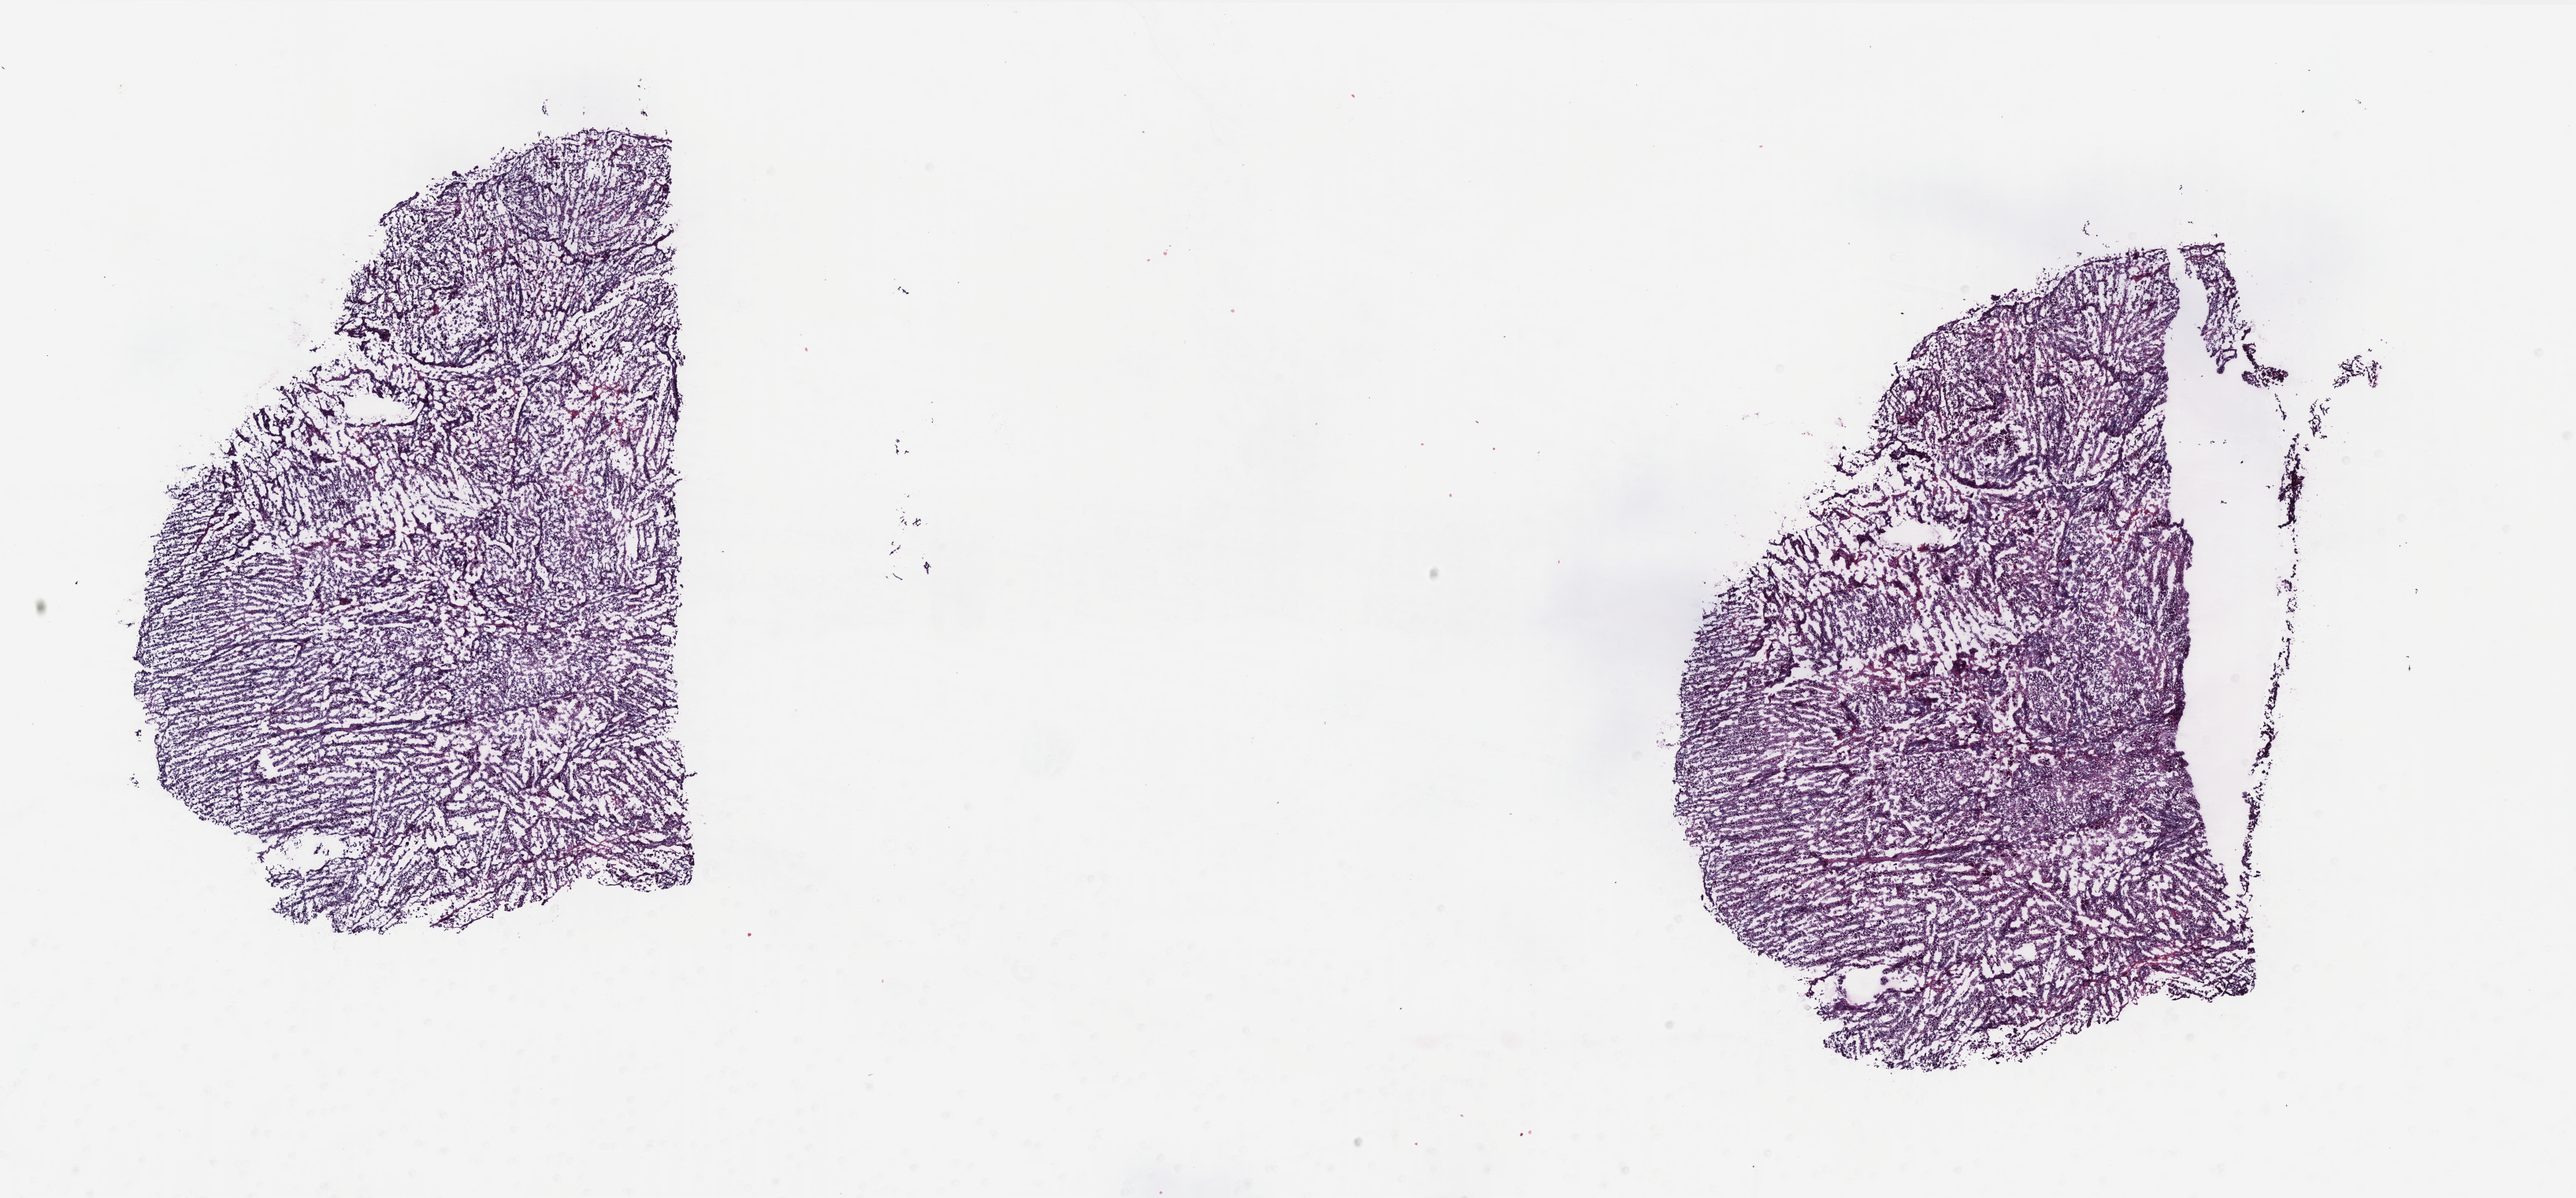
H&E whole-slide image — a low-resolution overview of the entire scanned area, about 26.2 x 12.2 mm. Frozen section from the top of the tissue portion. Uterus, primary tumour sample. Patient sex: female. Histologic grade: G3 (poorly differentiated). Pathologist review of this section (percent, as recorded): tumour cells 100%, tumour nuclei 60%, normal cells 0%, stromal cells 0%, necrosis 0%. Inflammatory infiltration, as recorded: lymphocyte infiltration 0%, monocyte infiltration 0%, neutrophil infiltration 0%.
FIGO stage: IVB. Diagnosis: Endometrioid adenocarcinoma, NOS (endometrium).